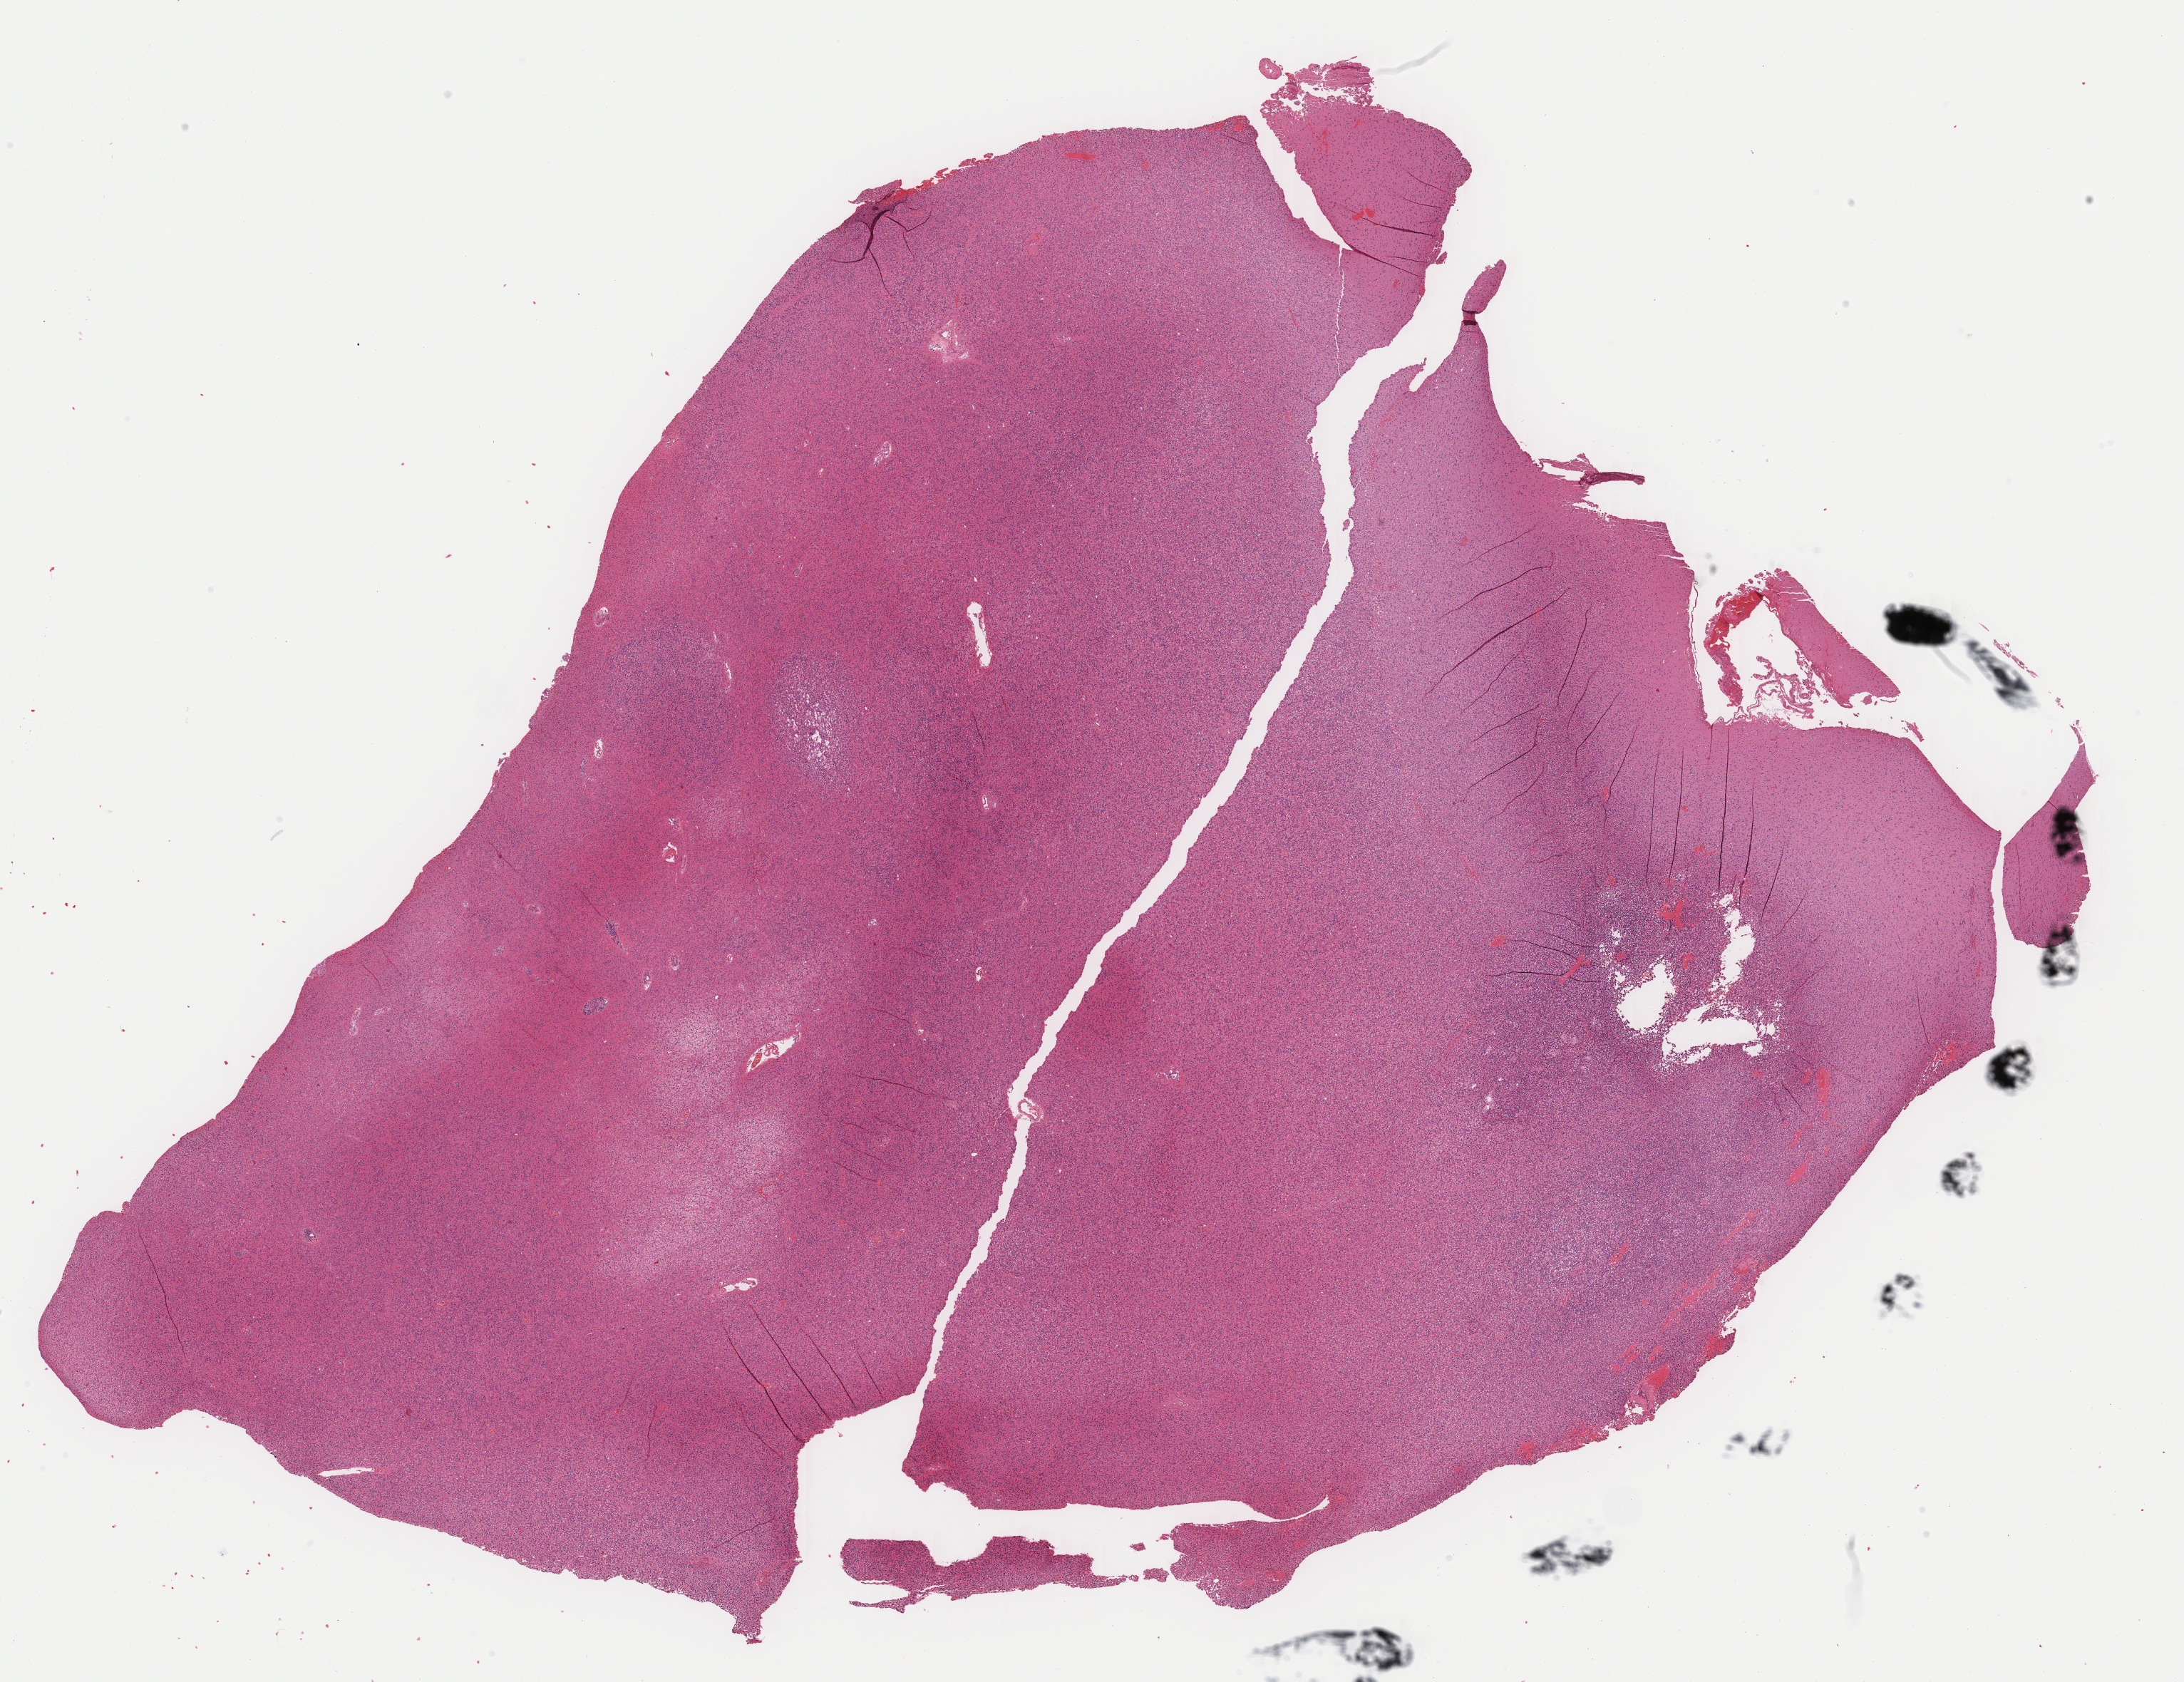
H&E-stained whole-slide image, low-resolution overview of the scanned area, about 24.1 x 18.6 mm. Formalin-fixed paraffin-embedded (FFPE) diagnostic section. Sample: primary tumour, brain. Patient: male, age at initial diagnosis 43 years. Histologic grade: G2 (moderately differentiated).
Pathologic diagnosis: Mixed glioma (cerebrum). Laterality: right.